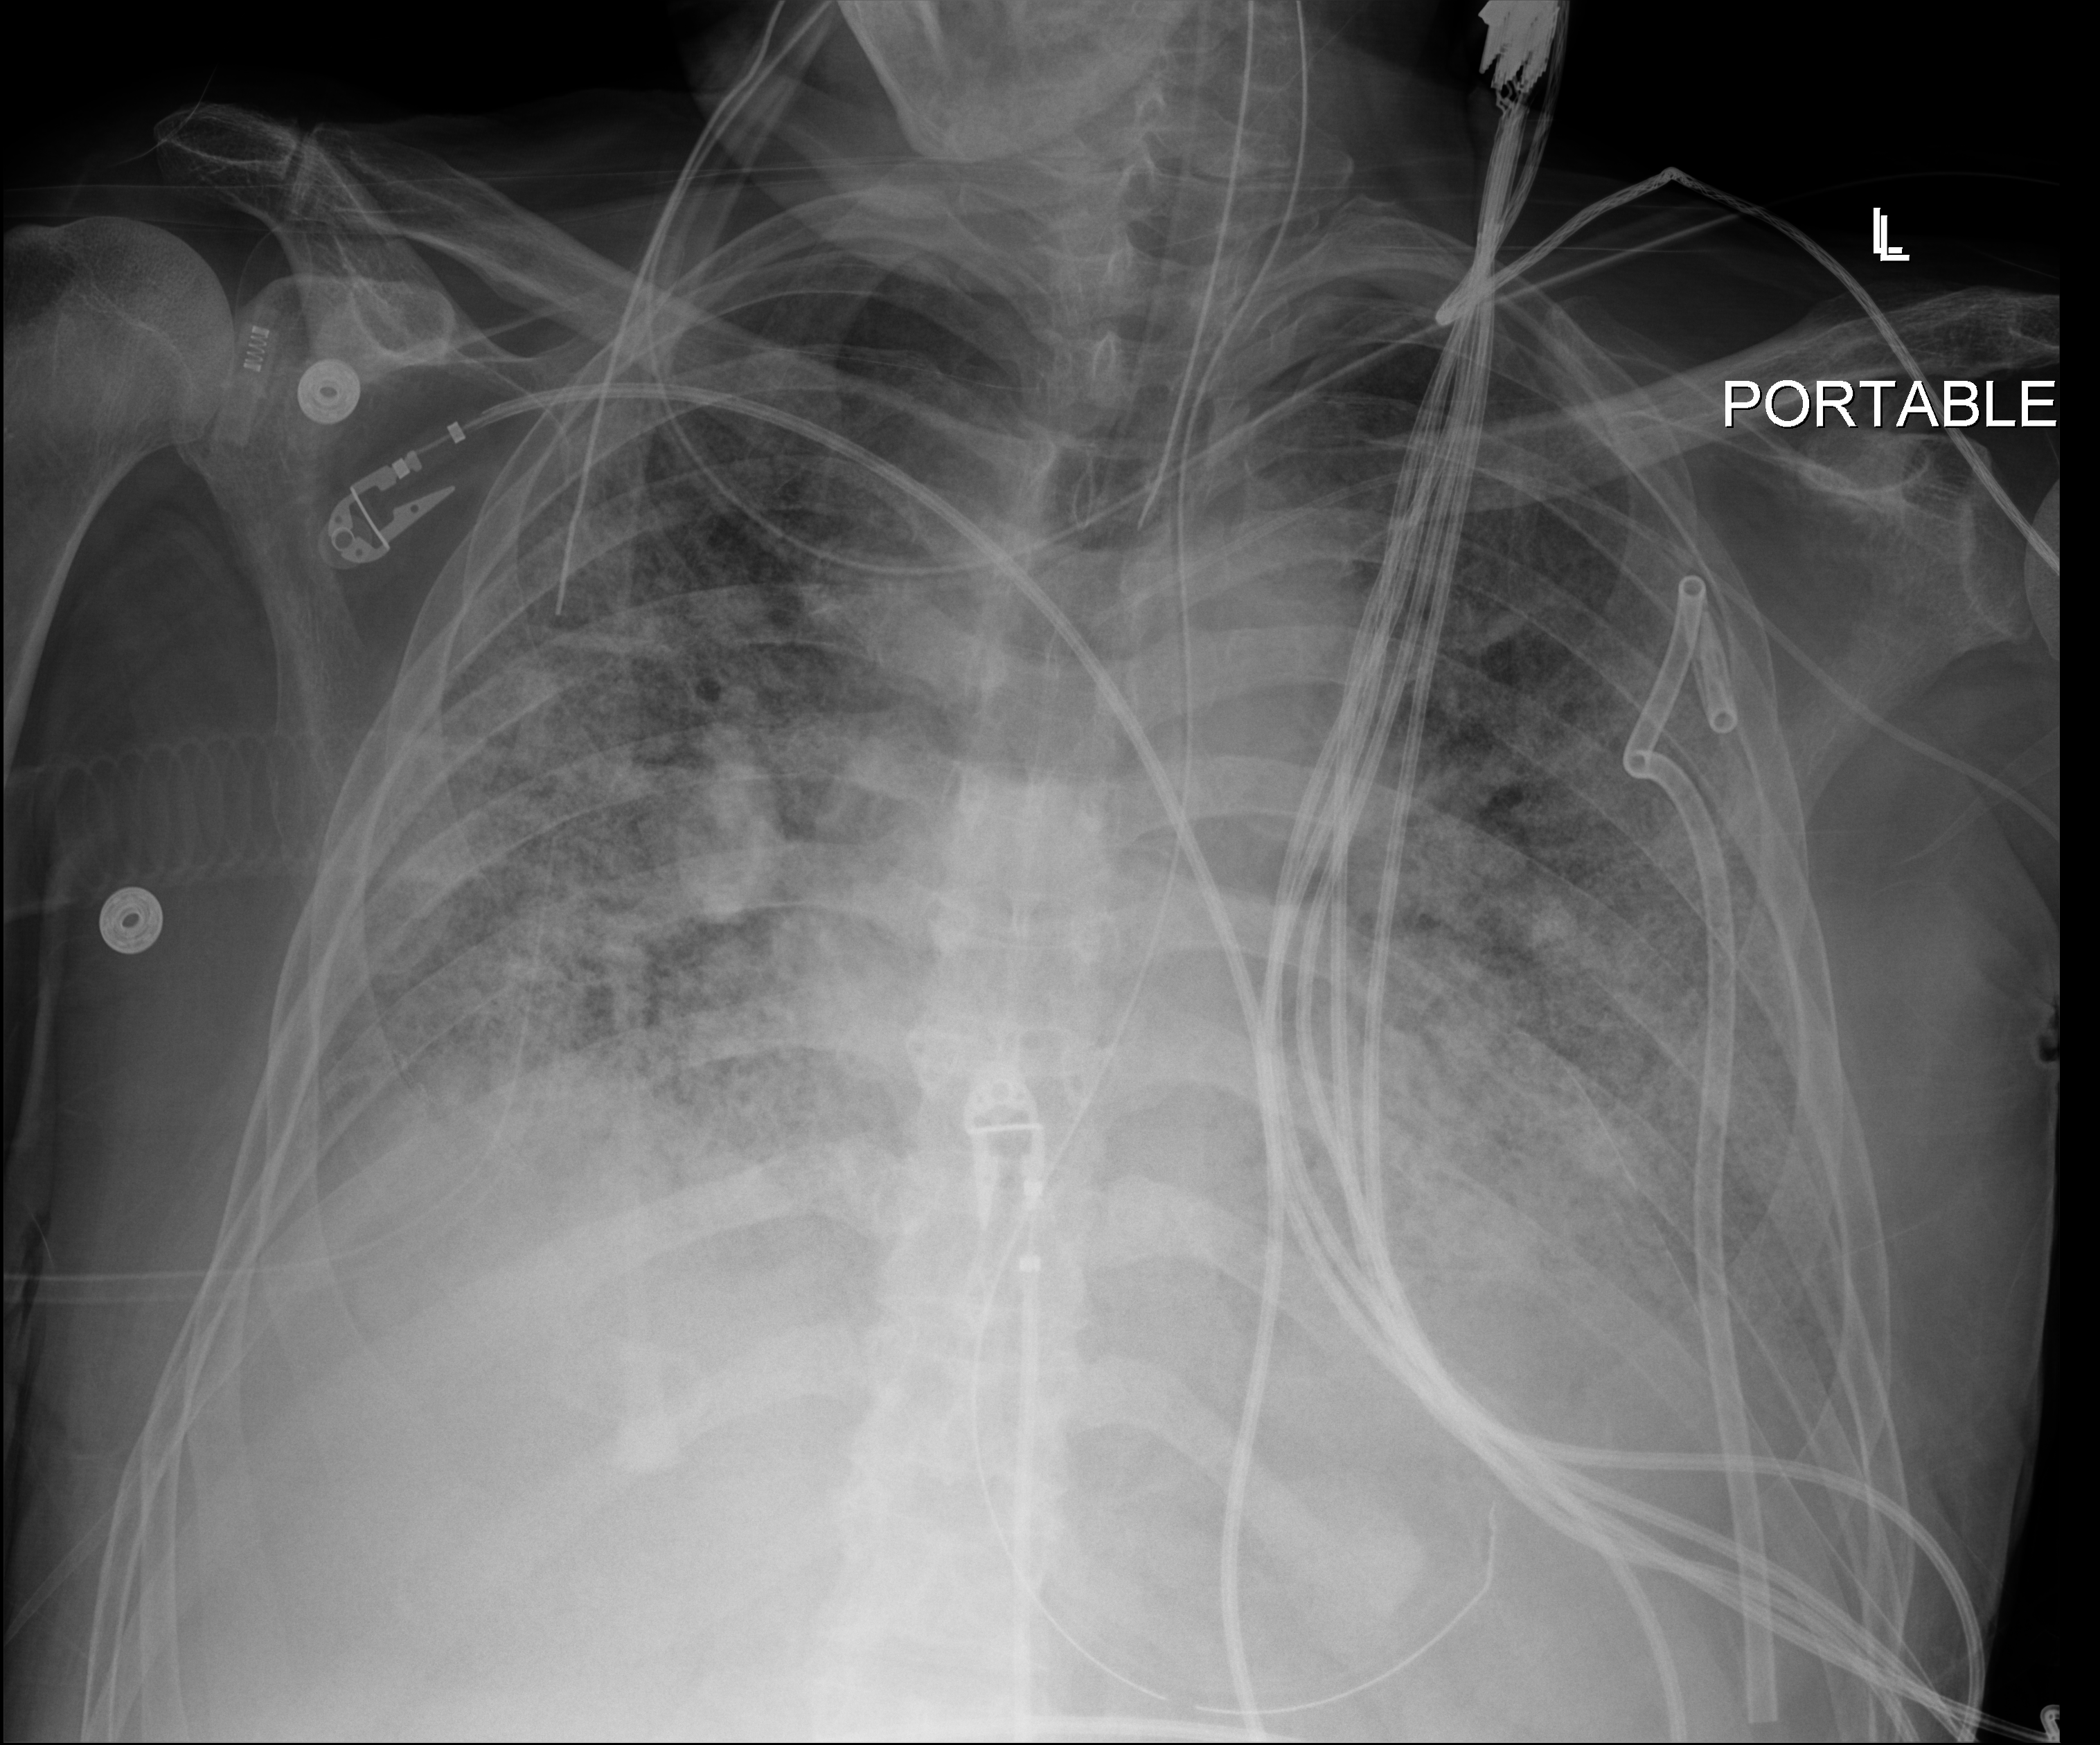
Bedside chest radiograph (digital radiography), anteroposterior (AP) projection. Patient hospitalised with COVID-19; male, aged 60–74 years.
From the hospital-stay record, not from the radiograph (when in the stay this image was taken is not recorded): admitted to intensive care during this hospital stay: yes.